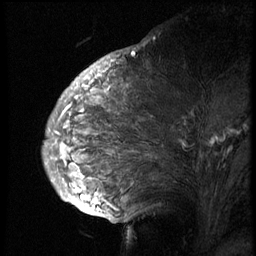
Breast MRI (dynamic contrast-enhanced), one sagittal slice; position 32 of 74 along the scan axis; 3 images stored at this slice position (order not interpretable as contrast timing); 1.5 T; TE 4.2 ms, TR 8.9 ms; 256 × 256 image matrix, field of view 200 × 200 mm. Patient: female, 57 years. From the clinical record (not read from this slice): setting: breast cancer imaged before/during neoadjuvant chemotherapy; receptor status: HER2-positive.
Annotated regions visible in this slice (semi-automatic segmentation, software-assisted and operator-edited):
- analysis volume of interest (the breast-tissue region the enhancement analysis was run in; not a lesion): box from (x=51, y=67) to (x=249, y=173) px
- tumour enhancement mask (voxels above the 140 % enhancement threshold inside the analysis volume of interest): (x=64, y=88)–(x=112, y=113)